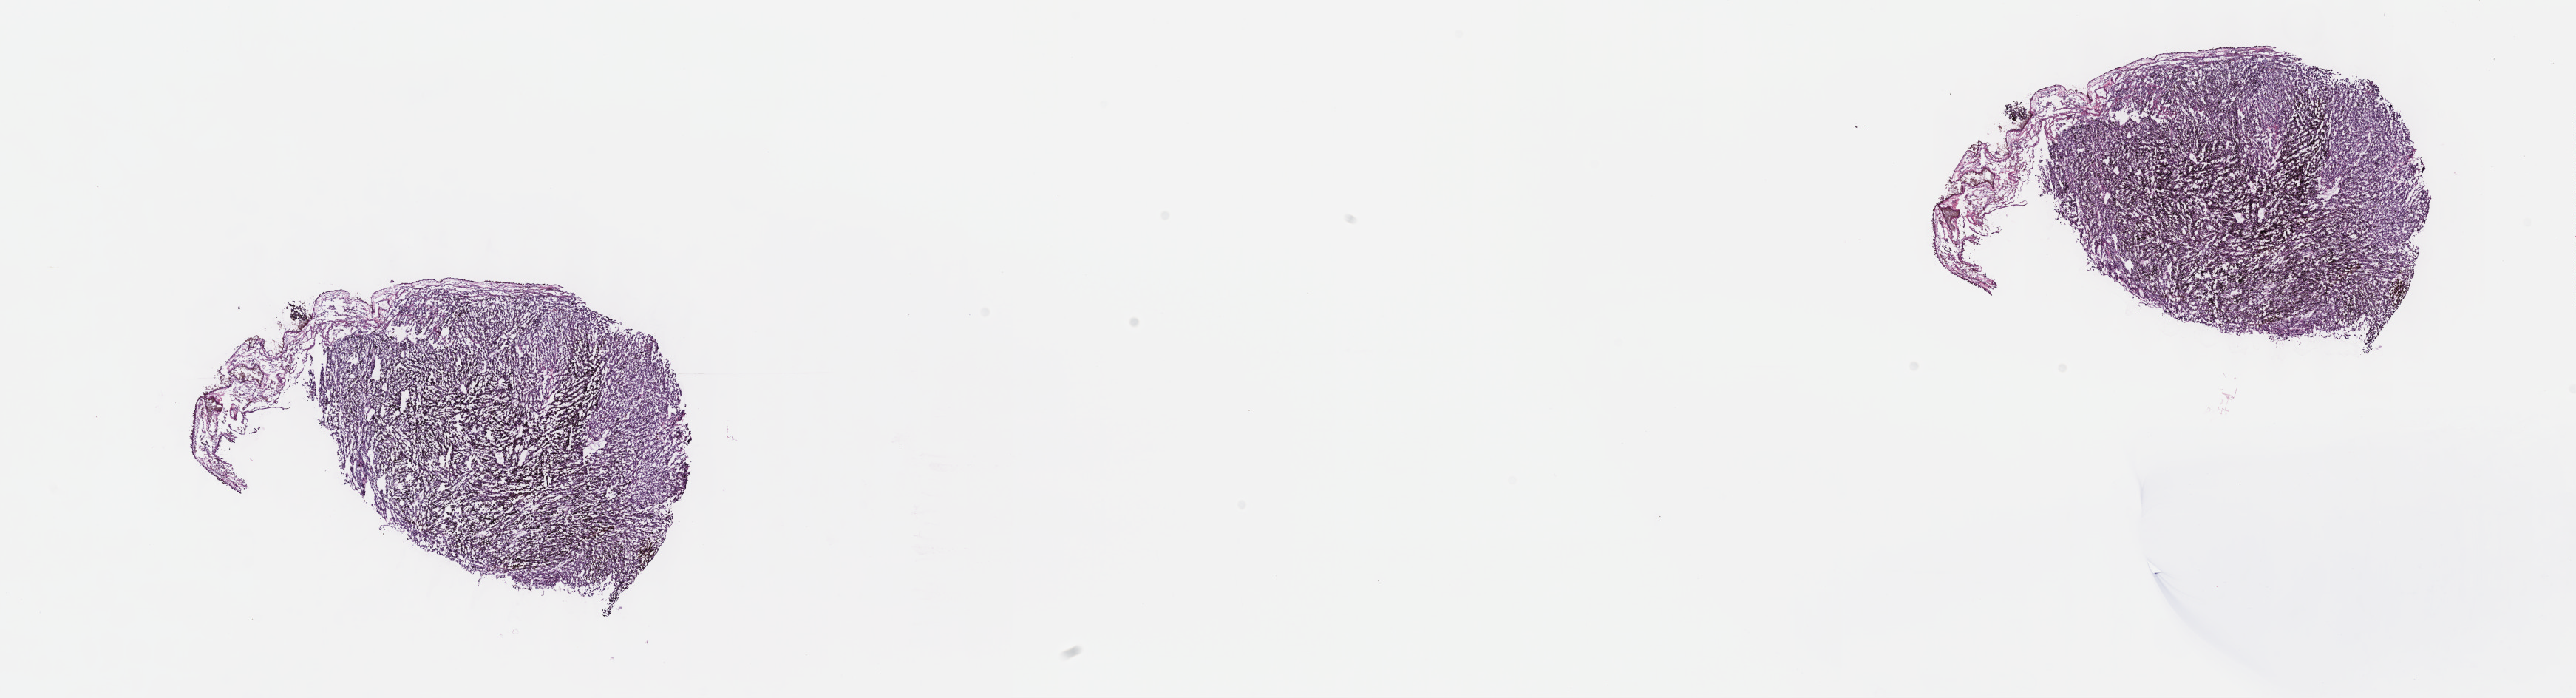
Digitized H&E tissue section (whole slide) — low-resolution overview of the scanned area, about 28.2 x 7.6 mm (slide scanned at 40x); frozen section; primary tumour sample from the uvea. Female patient; age at initial diagnosis 77 years. Composition of this section per pathologist review: tumour cells 100%, tumour nuclei 80%, normal cells 0%, stromal cells 0%, necrosis 0%. Inflammatory infiltration, as recorded: lymphocyte infiltration 1%, monocyte infiltration 0%, neutrophil infiltration 0%.
TNM: T3a NX MX. Histologic diagnosis: Mixed epithelioid and spindle cell melanoma (choroid). AJCC pathologic stage: IIB (7th edition).